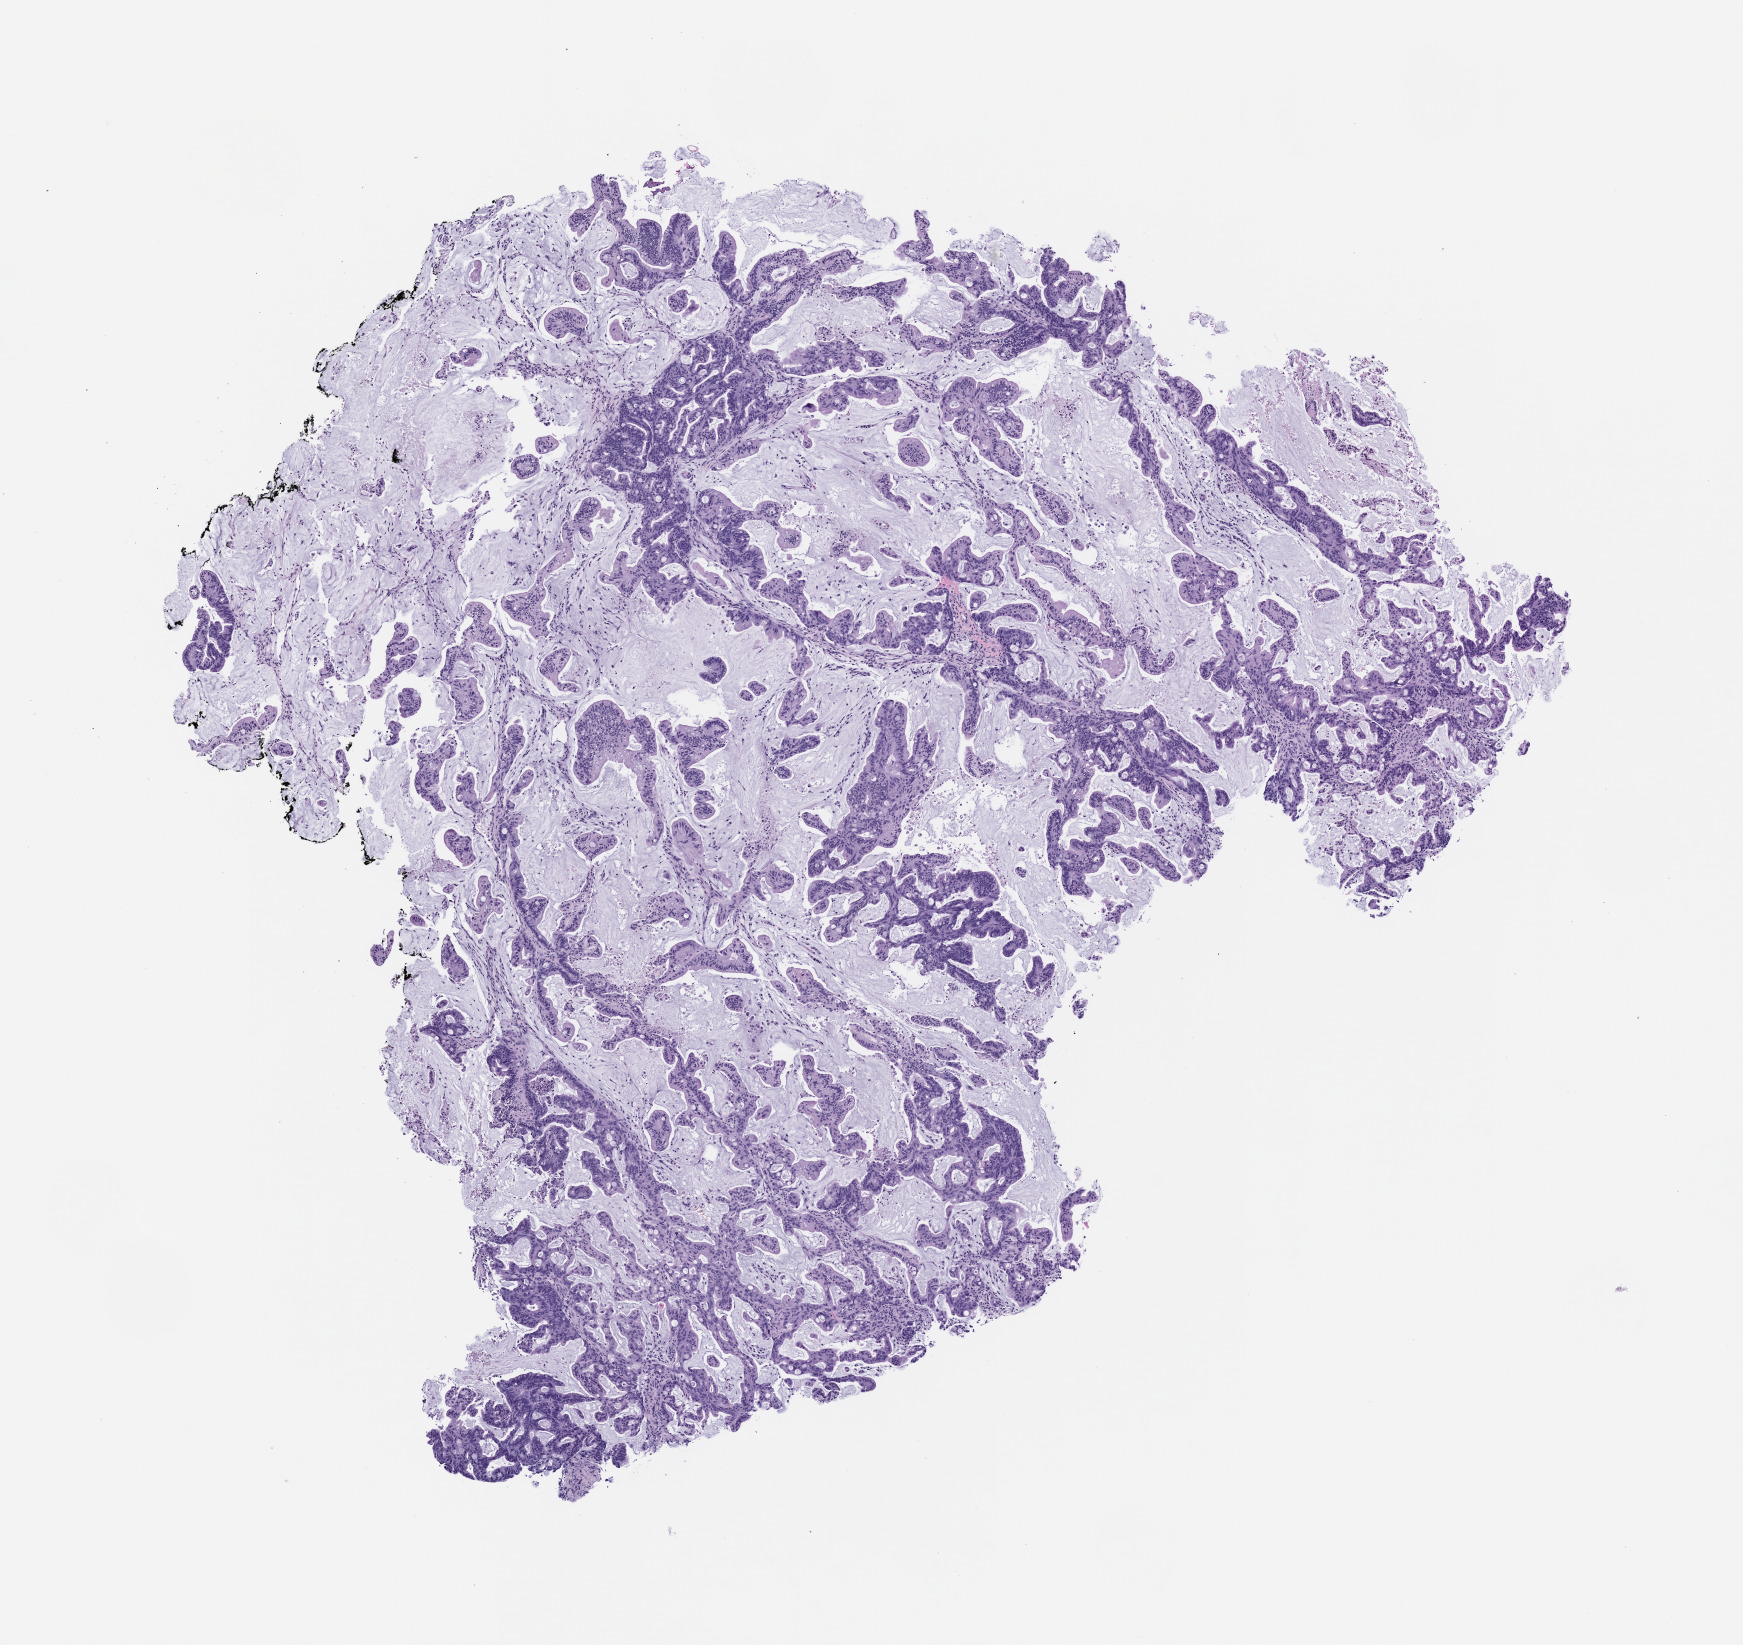
Hematoxylin and eosin (H&E) whole-slide image of a patient-derived xenograft (PDX) tumor grown in a mouse, passage 2, a low-resolution overview of the entire scanned area, about 7.0 x 6.6 mm, FFPE section, tumor site category: rectum.
- originating patient diagnosis: Rectal Adenocarcinoma